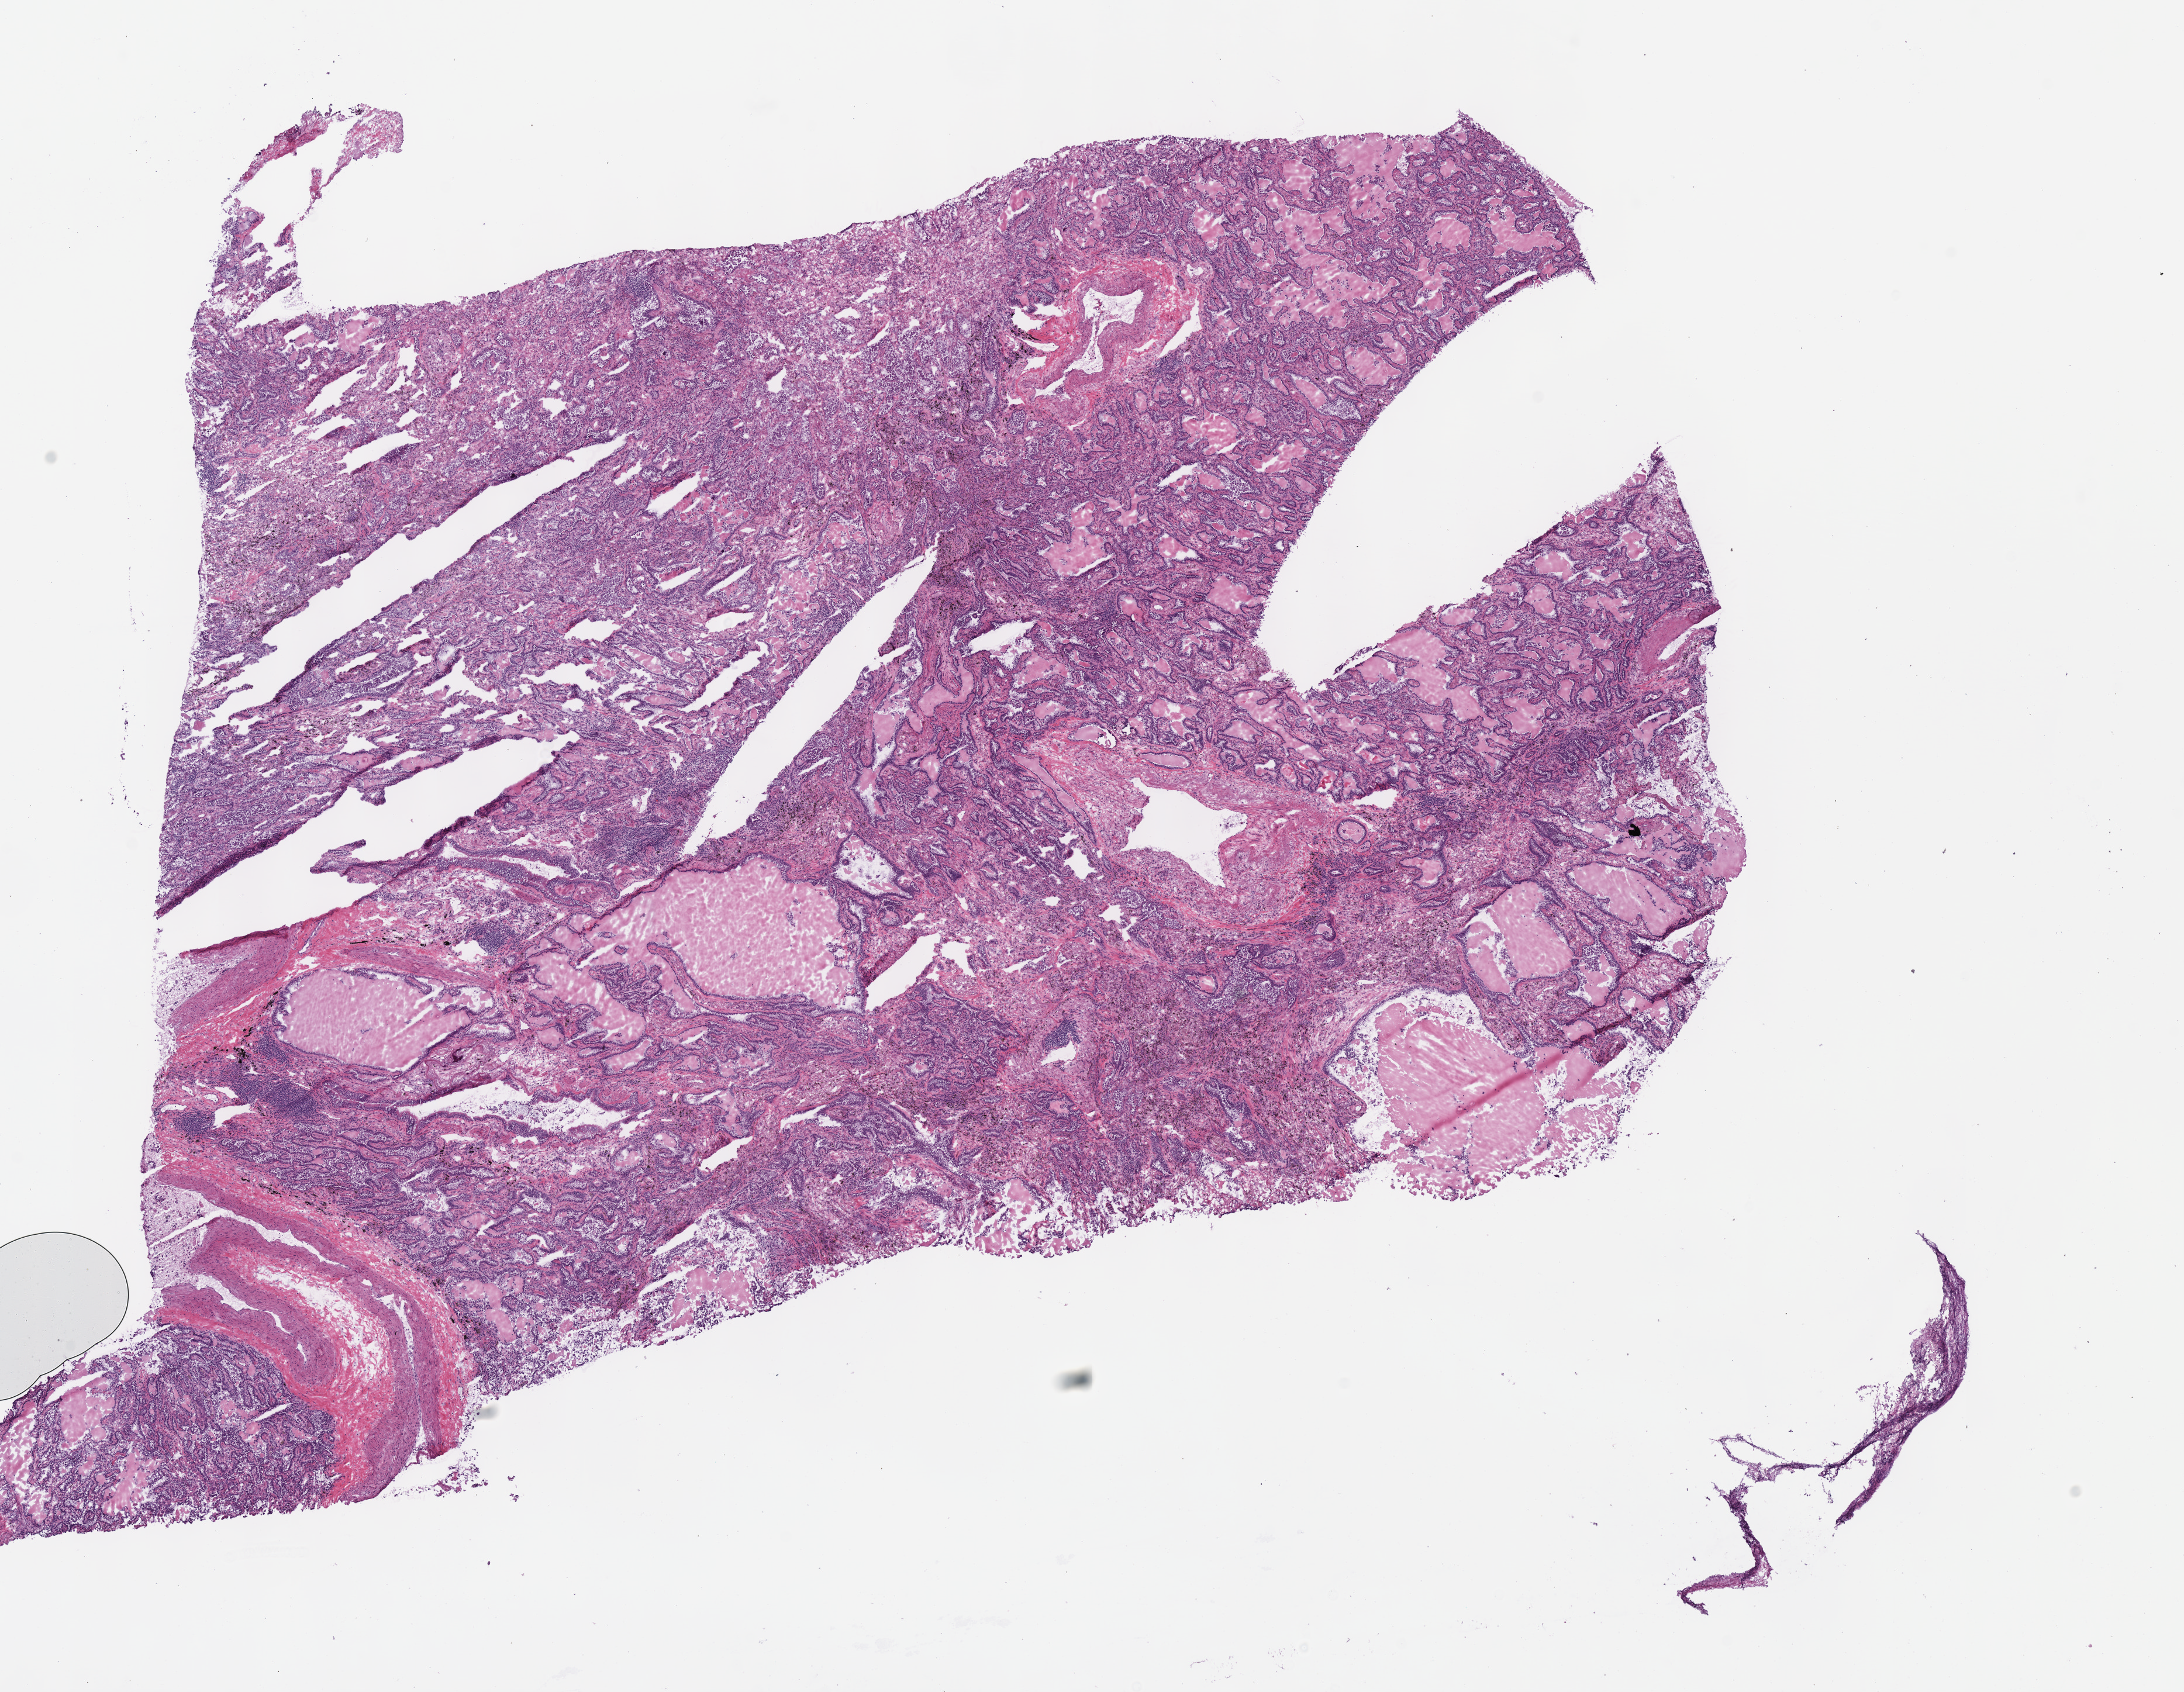
H&E-stained whole-slide image — low-resolution overview of the scanned area, about 14.7 x 11.4 mm (from a 40x scan). Frozen section from the bottom of the tissue portion. Sample: primary tumour, lung. Patient: male, age at initial diagnosis 70 years. Slide review estimates, as recorded: tumour cells 80%, tumour nuclei 60%, normal cells 0%, stromal cells 20%, necrosis 0%.
Histologic diagnosis: Adenocarcinoma, NOS (upper lobe, lung). AJCC pathologic stage: IA (7th edition). Laterality: left.